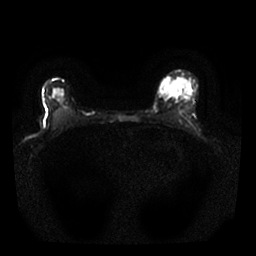
Breast MRI, one axial slice. Position 17 of 25 along the scan axis. Diffusion-weighted series; image 2 of 4 stored at this slice position (different b-values; order by instance number). 1.5 T. 4 mm slice thickness. 256 × 256 image matrix, field of view 310 × 310 mm. Female patient.
Structures marked on this image (manually delineated by an expert):
- tumour on diffusion-weighted imaging: bounding box (x1, y1, x2, y2) in pixels: (160, 80, 181, 97)